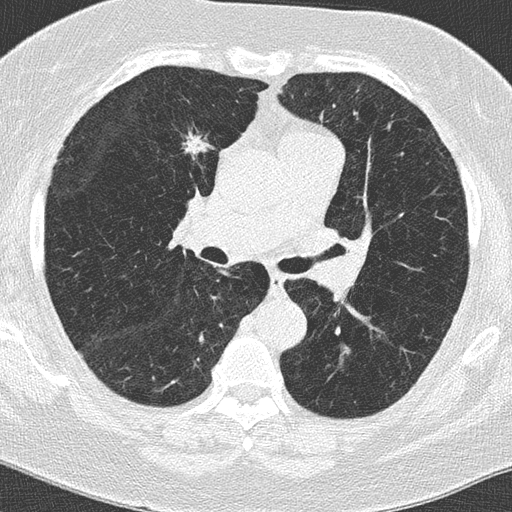
Low-dose screening chest CT, axial slice; second annual screen; lung window (W 1500 / L -600 HU); 2 mm slice thickness; slice 60 of 152 in the series. Female, age 62 years at enrolment.
- Expert-annotated lung lesion, box from (x=160, y=115) to (x=228, y=174) px.
- The screening reader recorded 2 non-calcified nodules or masses ≥4 mm on this exam; which of them this box marks is not recorded.
- Later outcome: lung cancer diagnosed 396 days after this screen — adenocarcinoma, NOS, right upper lobe, moderately differentiated (G2), stage IA (AJCC 6th edition), 15 mm at pathology.